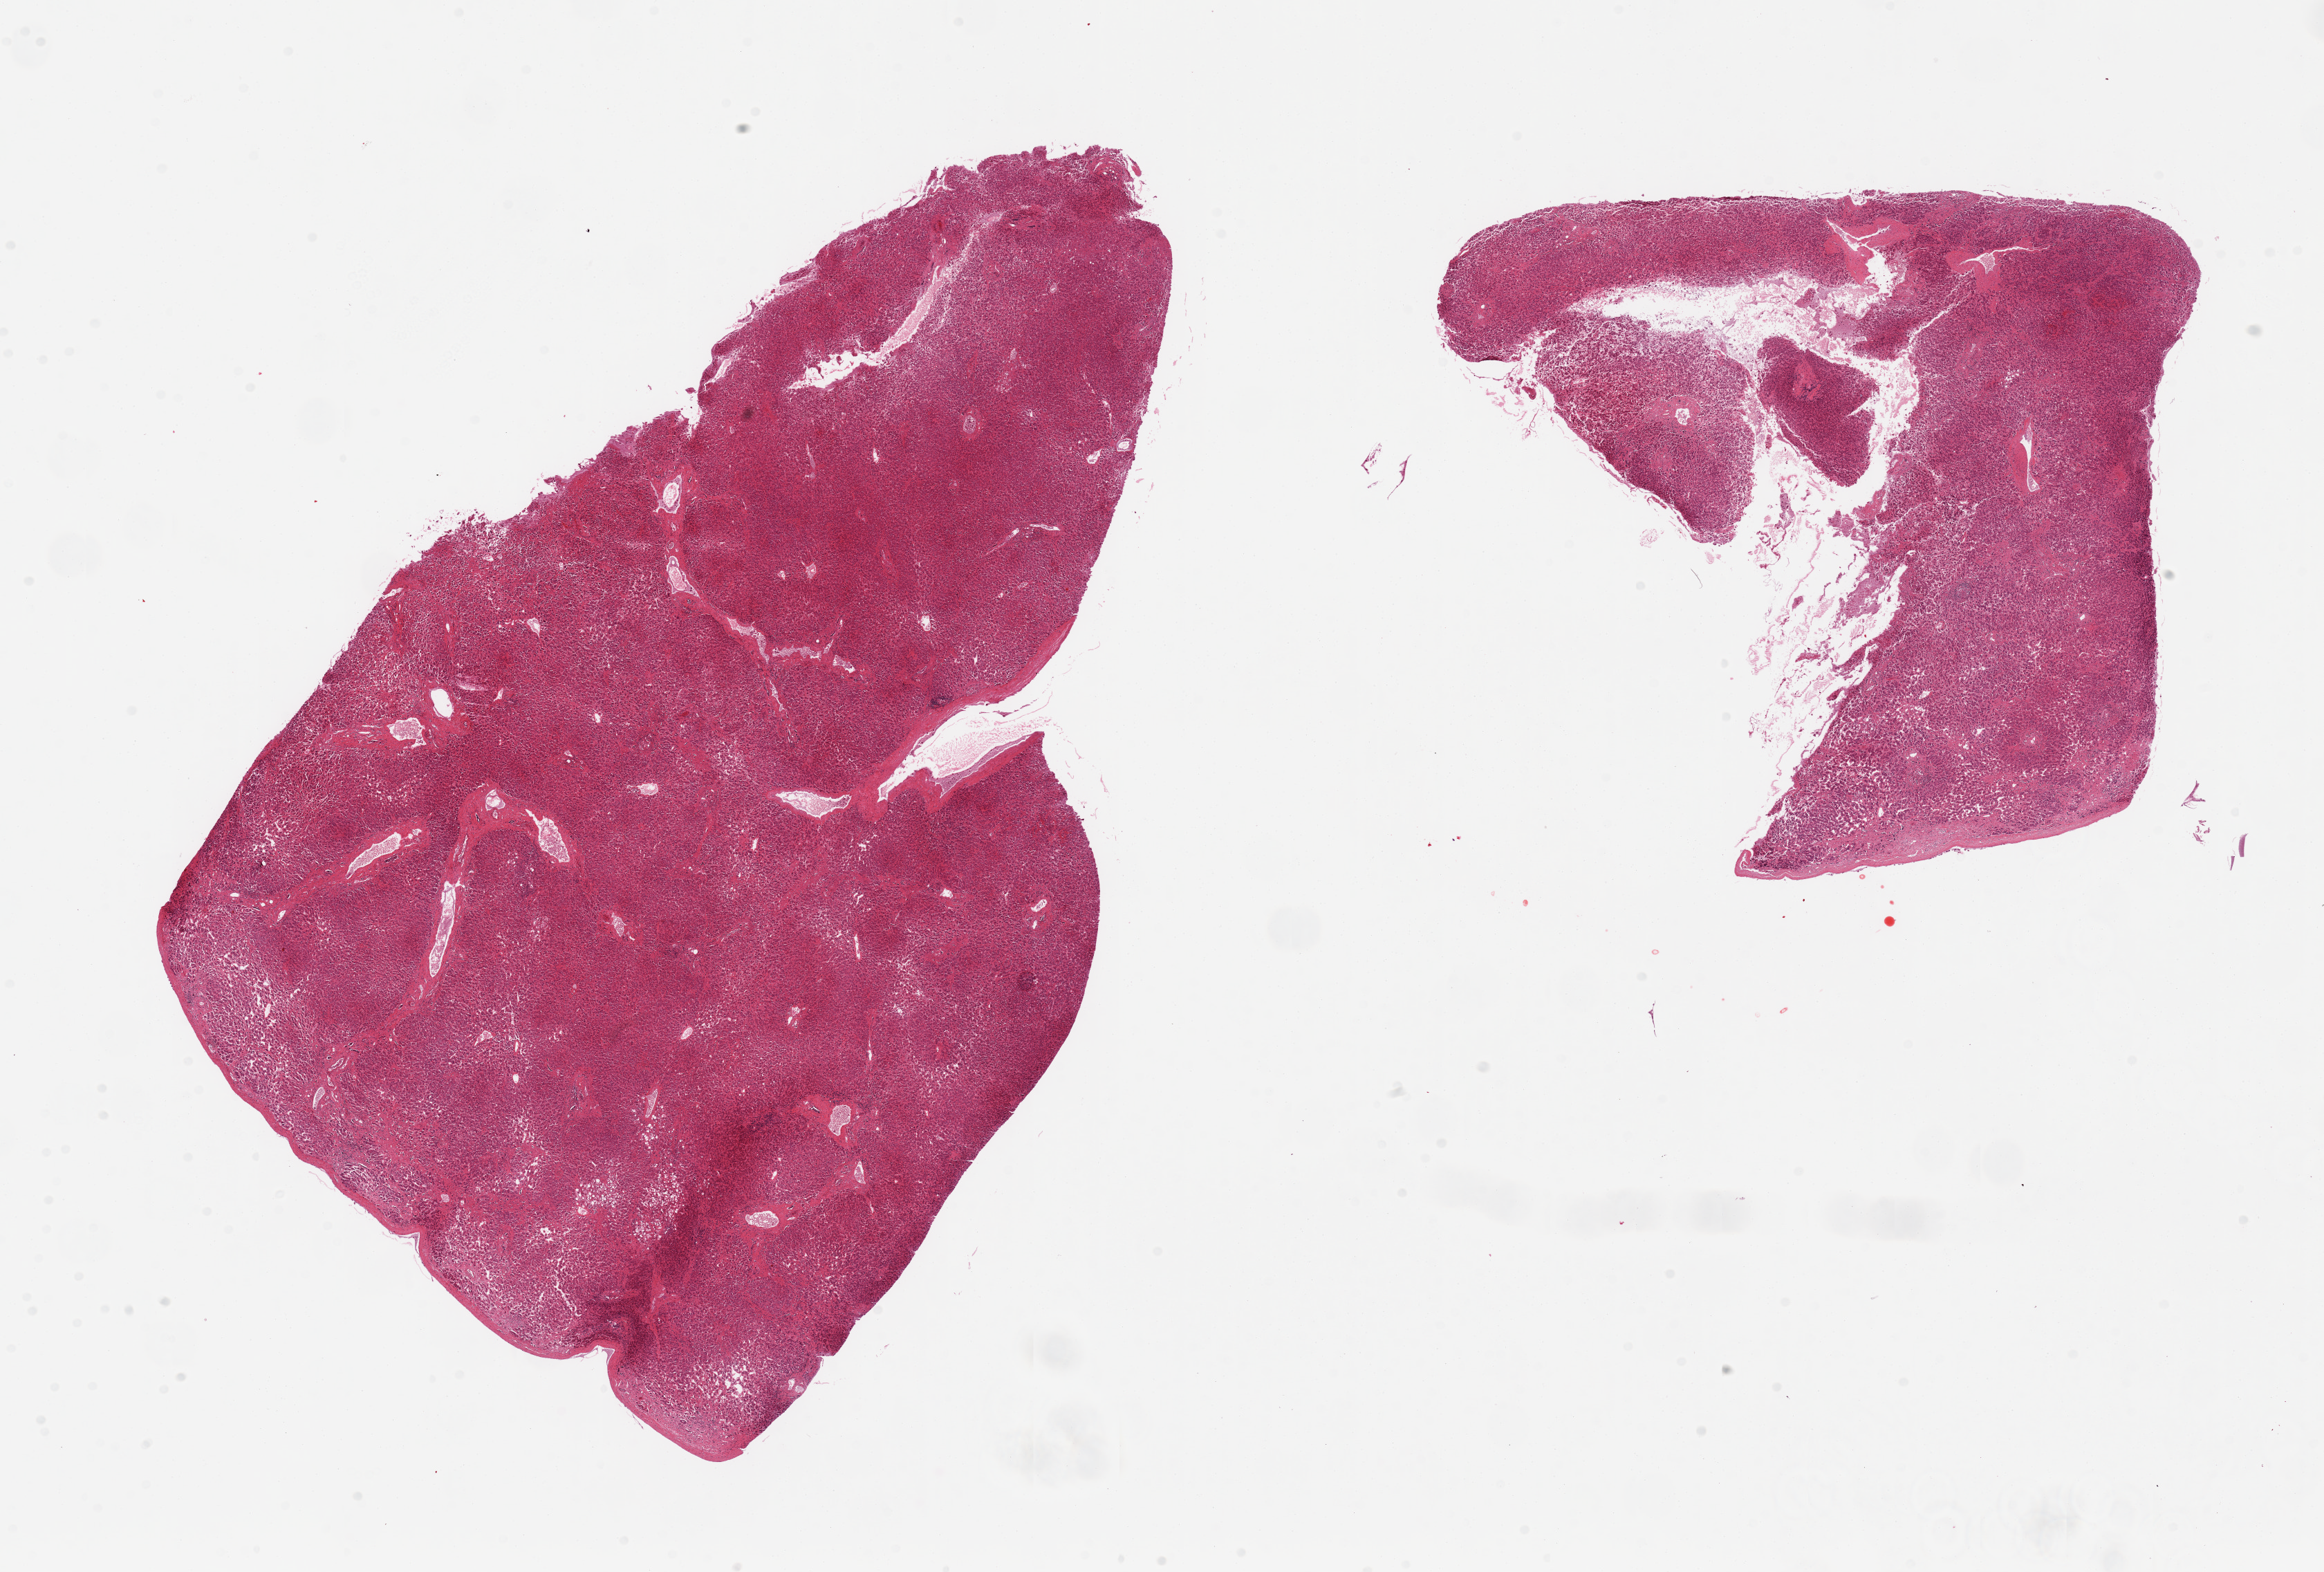
Digitized H&E-stained section — a low-resolution overview of the entire scanned area, about 26.6 x 18.0 mm; PAXgene-fixed, paraffin-embedded tissue; section of liver (target tissue); tissue donor sample. Male donor.
Pathologist's review note for this sample: 2 pieces, pathcy macrovesicular steatosis.